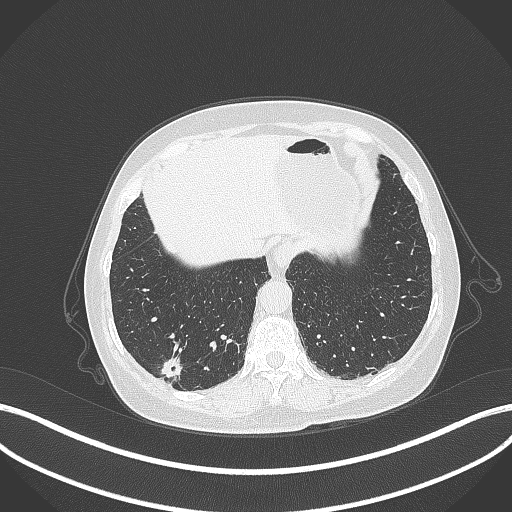
Chest CT, one axial slice; slice 56 of 333 in the series (ordered by position); 120 kVp; lung window (W 1500 / L -600 HU); 512 × 512 image matrix, field of view 400 × 400 mm. Patient: female, 69 years. From the clinical record (not read from this slice): clinical TNM (as recorded): T1b N0 M0.
Annotated regions visible in this slice (bounding box drawn by a radiologist):
- lung tumour (recorded histology: adenocarcinoma): bounding box (x1, y1, x2, y2) in pixels: (158, 354, 183, 382)